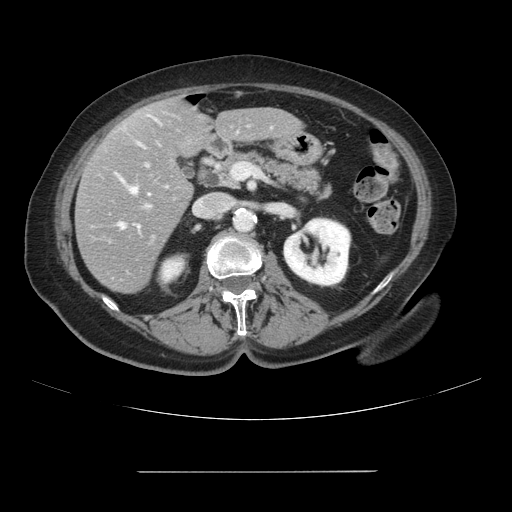
Contrast-enhanced abdominal CT, one axial slice. Slice 41 of 111 in the series (ordered by position). Intravenous contrast given. Soft-tissue window (W 400 / L 40 HU). 2.5 mm slice thickness. 512 × 512 image matrix, field of view 400 × 400 mm. Female patient, age 74 years. From the clinical record (not read from this slice): diagnosis: colorectal cancer liver metastases, imaged before liver resection; multiple liver metastases: yes; largest metastasis: 1.1 cm; chemotherapy before resection: yes.
Structures marked on this image (manually delineated by an expert):
- hepatic veins: bounding box [x1, y1, x2, y2] px = [119, 188, 137, 229]
- liver: [75, 99, 302, 293]
- planned liver remnant (the part of the liver to remain after resection): [140, 99, 302, 157]
- portal vein (with intrahepatic branches): [122, 181, 149, 208]